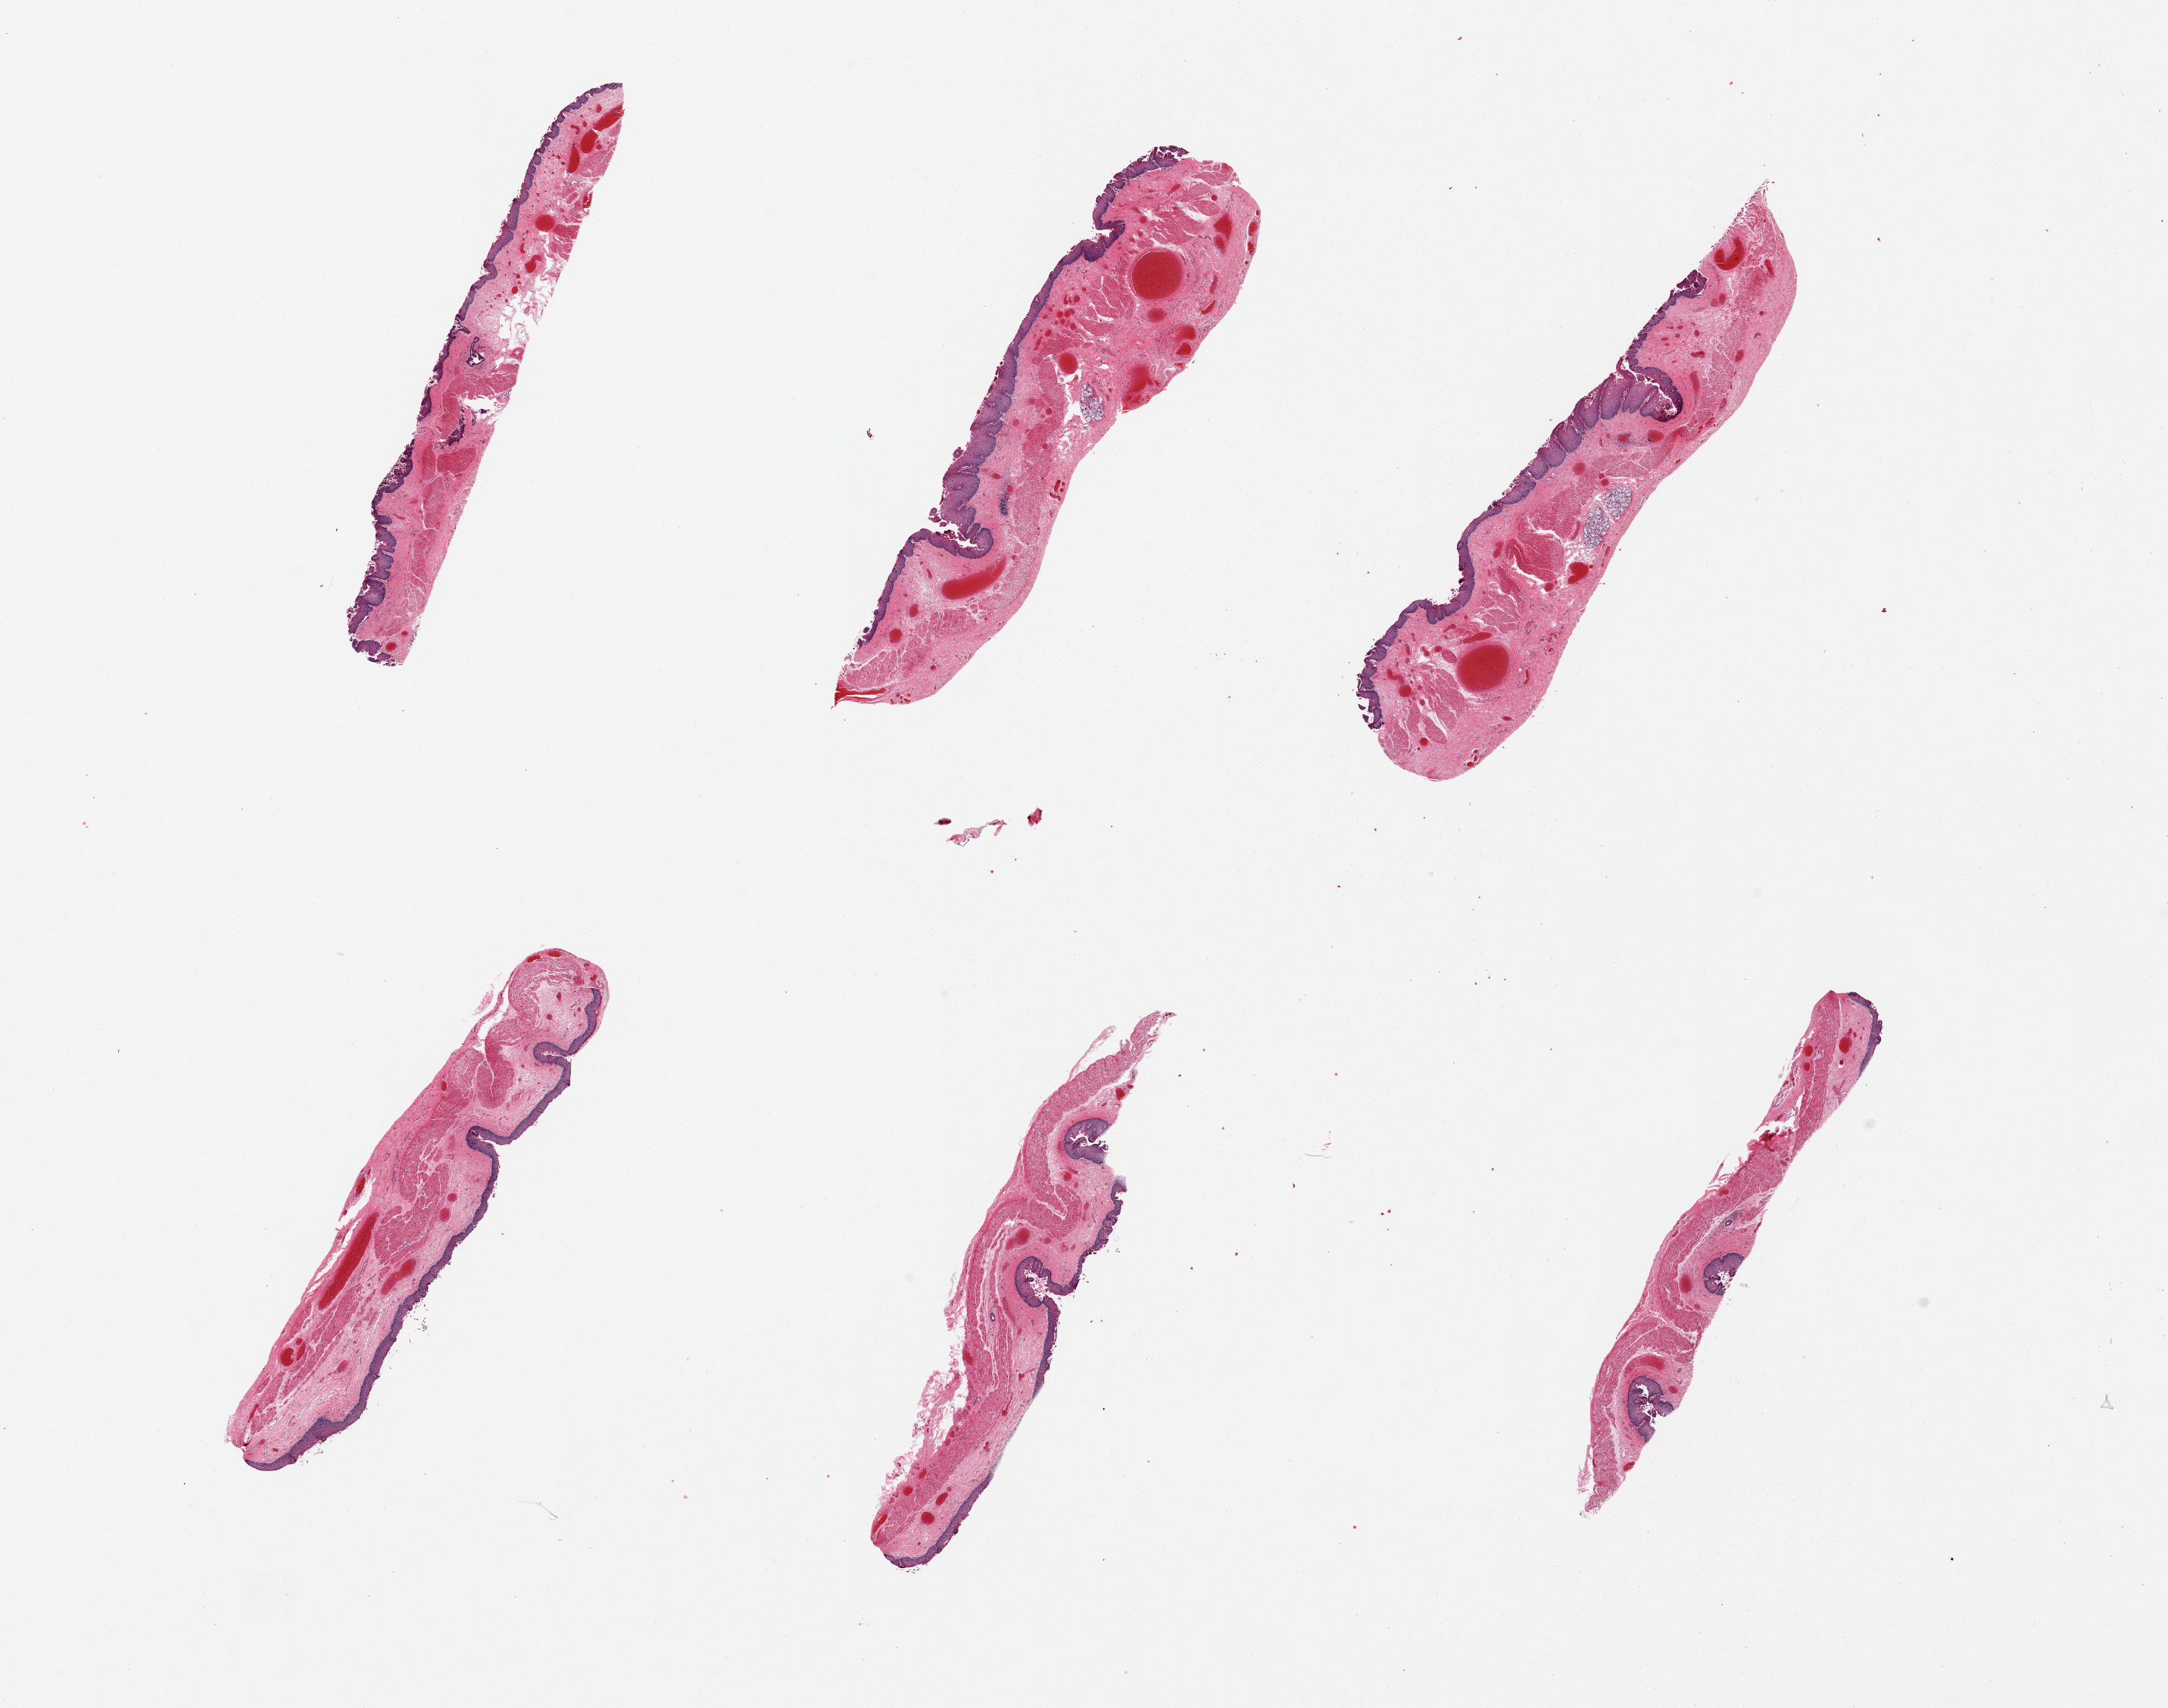
Whole-slide image, H&E stain — low-resolution overview of the scanned area, about 22.6 x 17.8 mm. PAXgene-fixed paraffin-embedded (PFPE) section. Section of esophageal mucous membrane (target tissue). Tissue donor sample. Donor: female.
Review note (as recorded): 6 pieces, squamous mucosa ~10-20% thickness, occasional submucosal mucus glands.